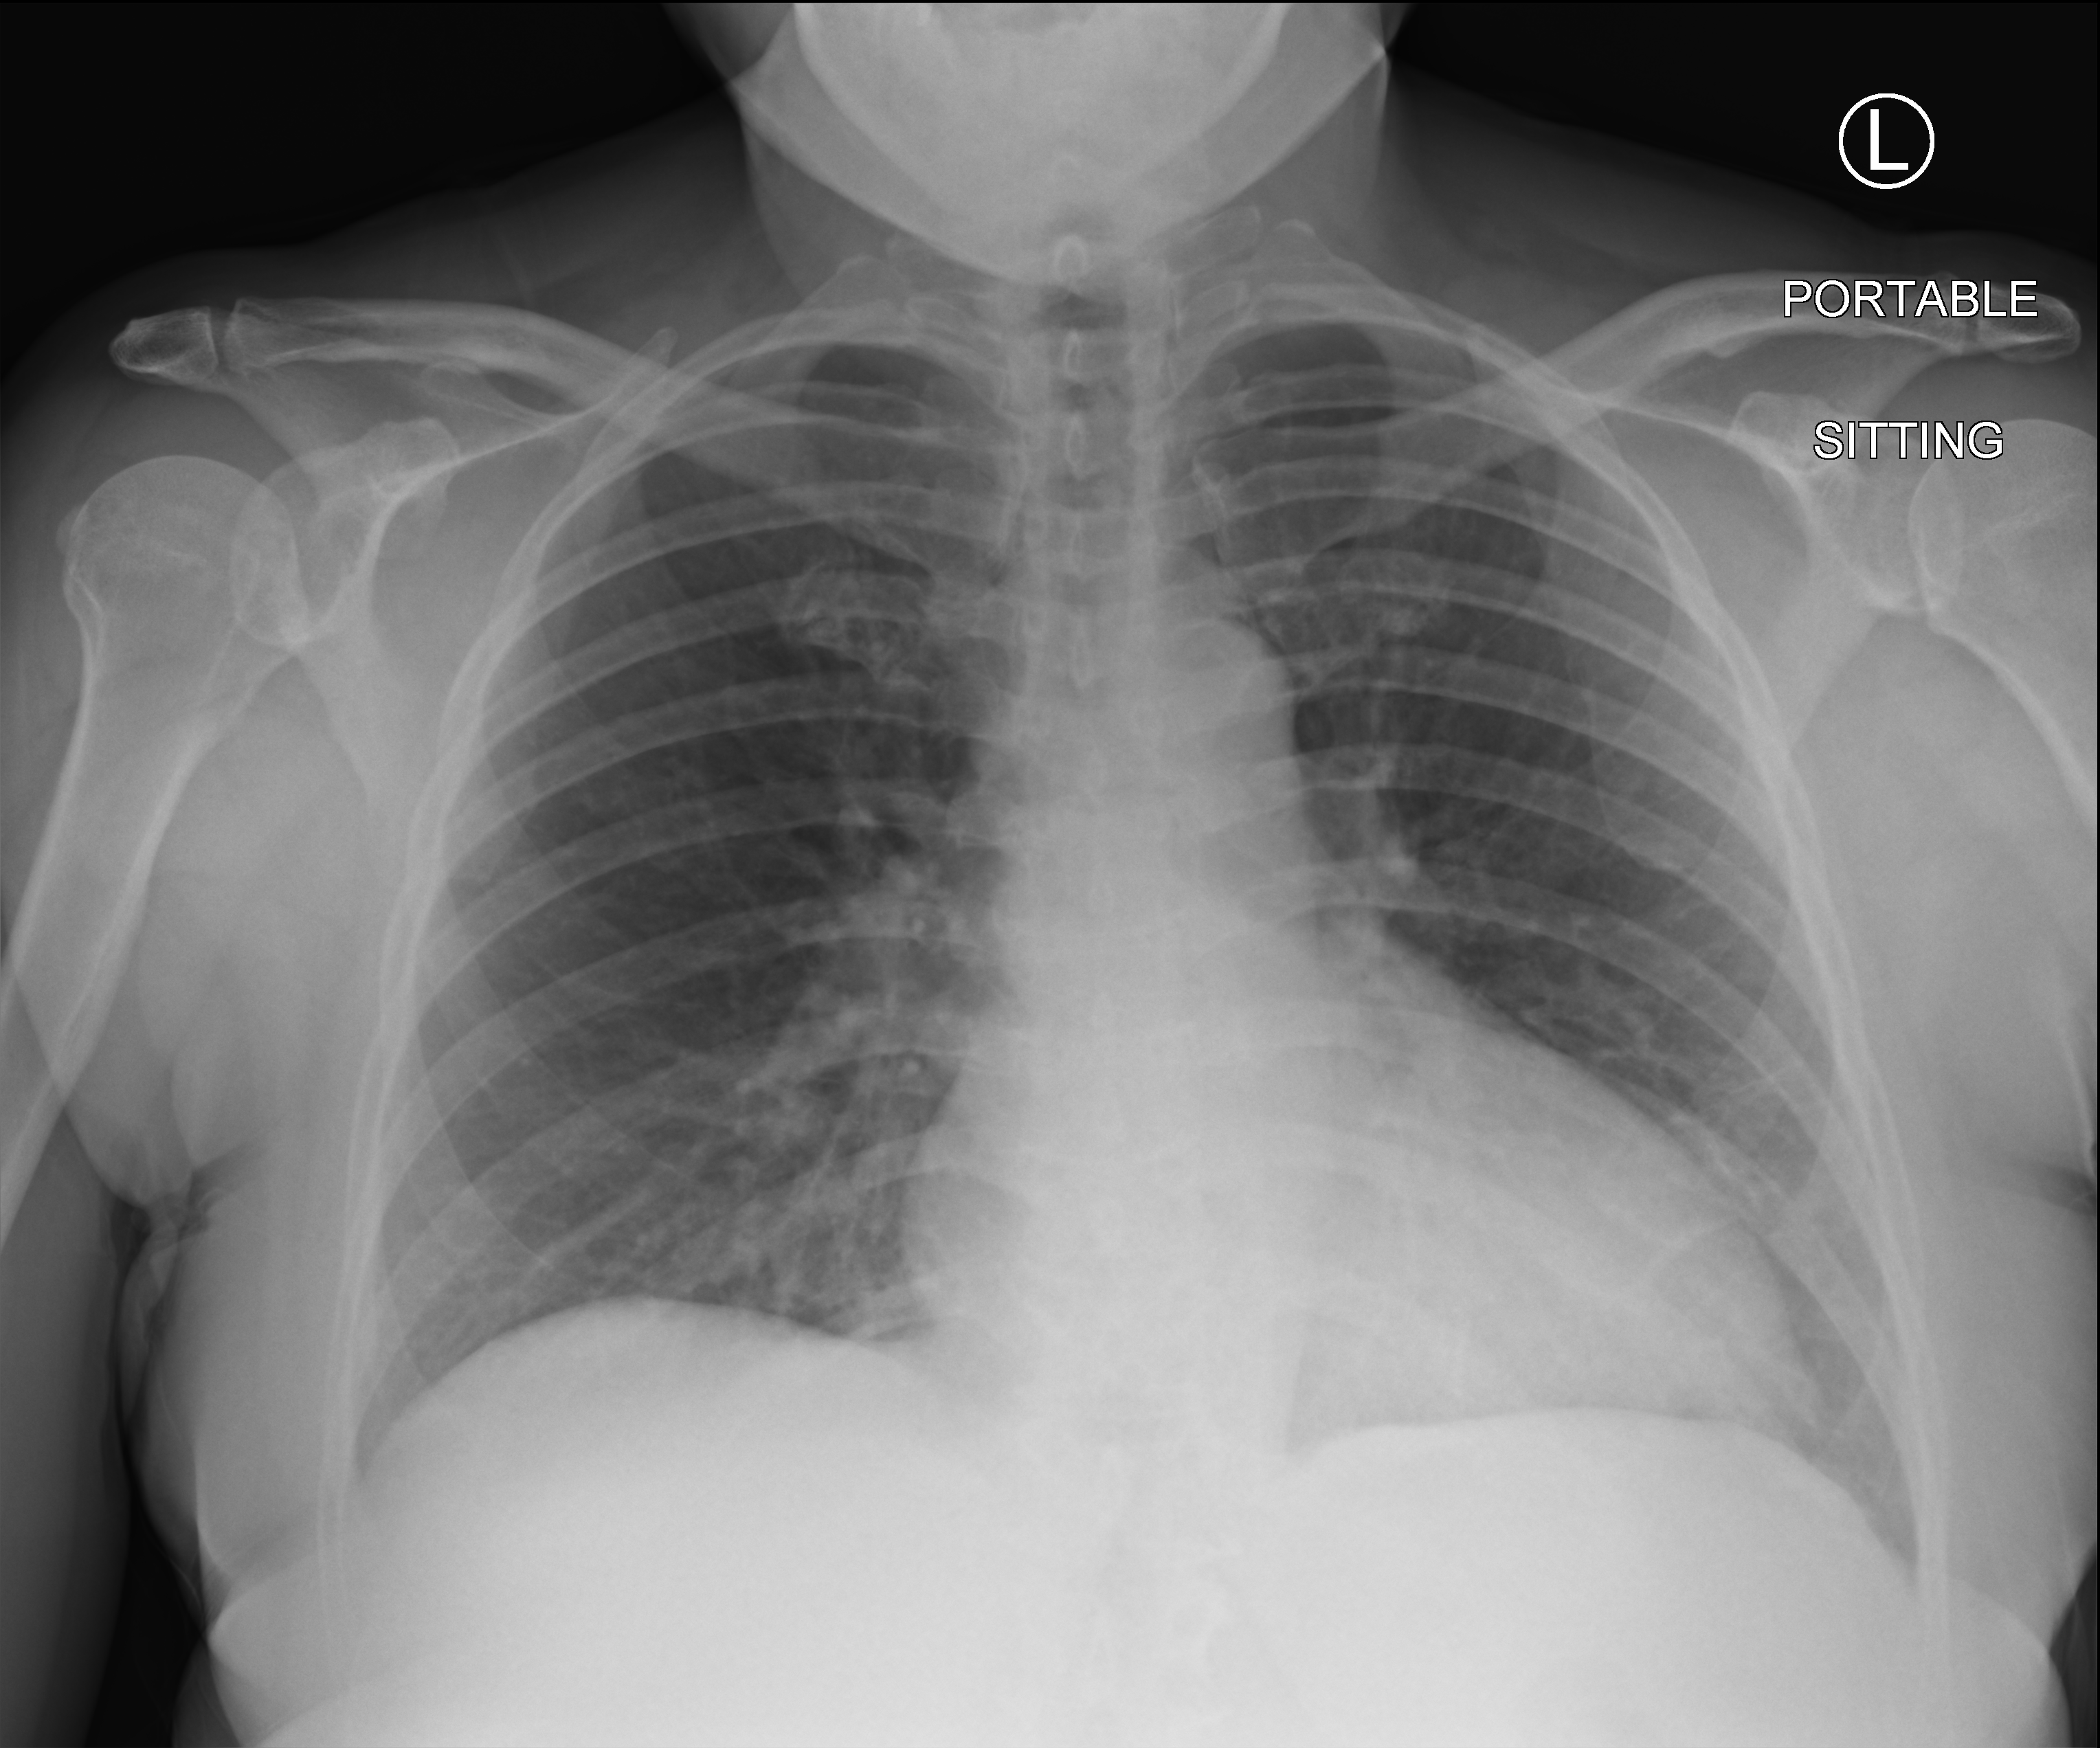
Bedside chest radiograph (computed radiography). Patient hospitalised with COVID-19; female, aged 60–74 years.
Hospital-stay facts (about this admission, not read from this image; timing relative to this image not recorded): chronic kidney disease (admission record): no; admitted to intensive care during this hospital stay: no.